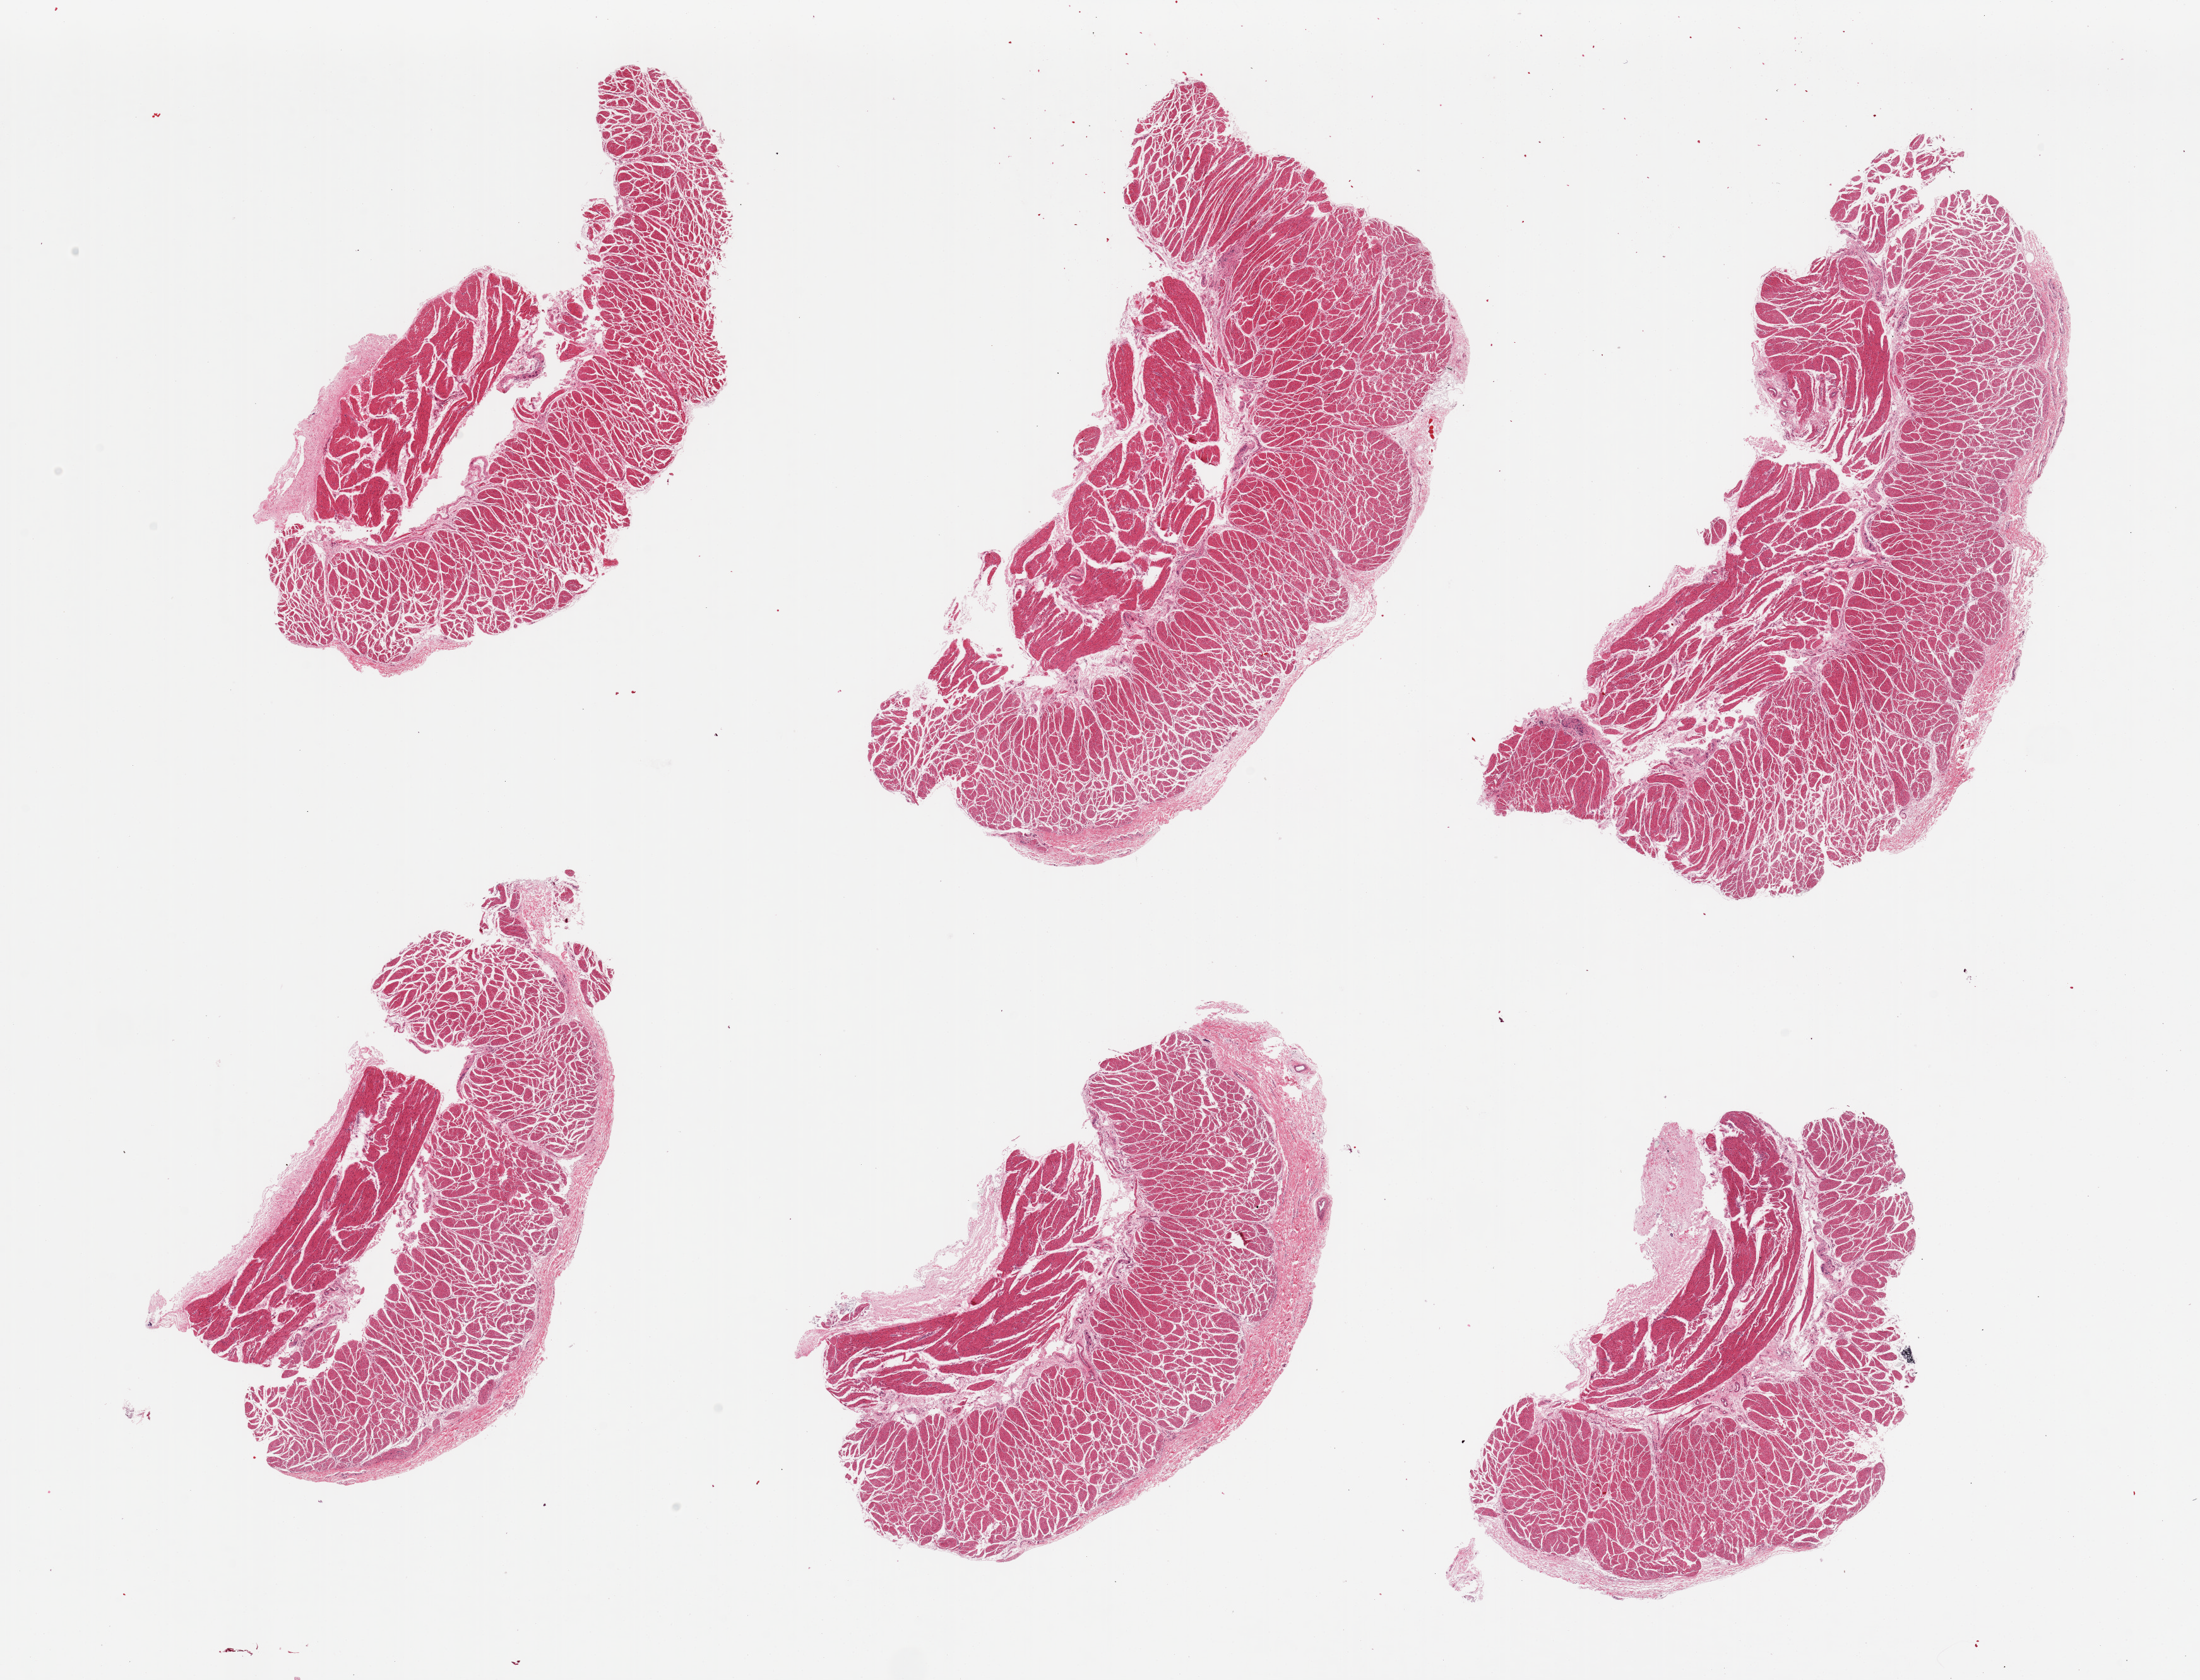
H&E whole-slide image, brightfield — whole scanned area (about 27.6 x 21.0 mm) shown as a low-resolution overview; PAXgene-fixed, paraffin-embedded tissue; section of esophageal muscle (target tissue); donor tissue sample.
* review note (as recorded): 6 pieces, well-trimmed of mucosa